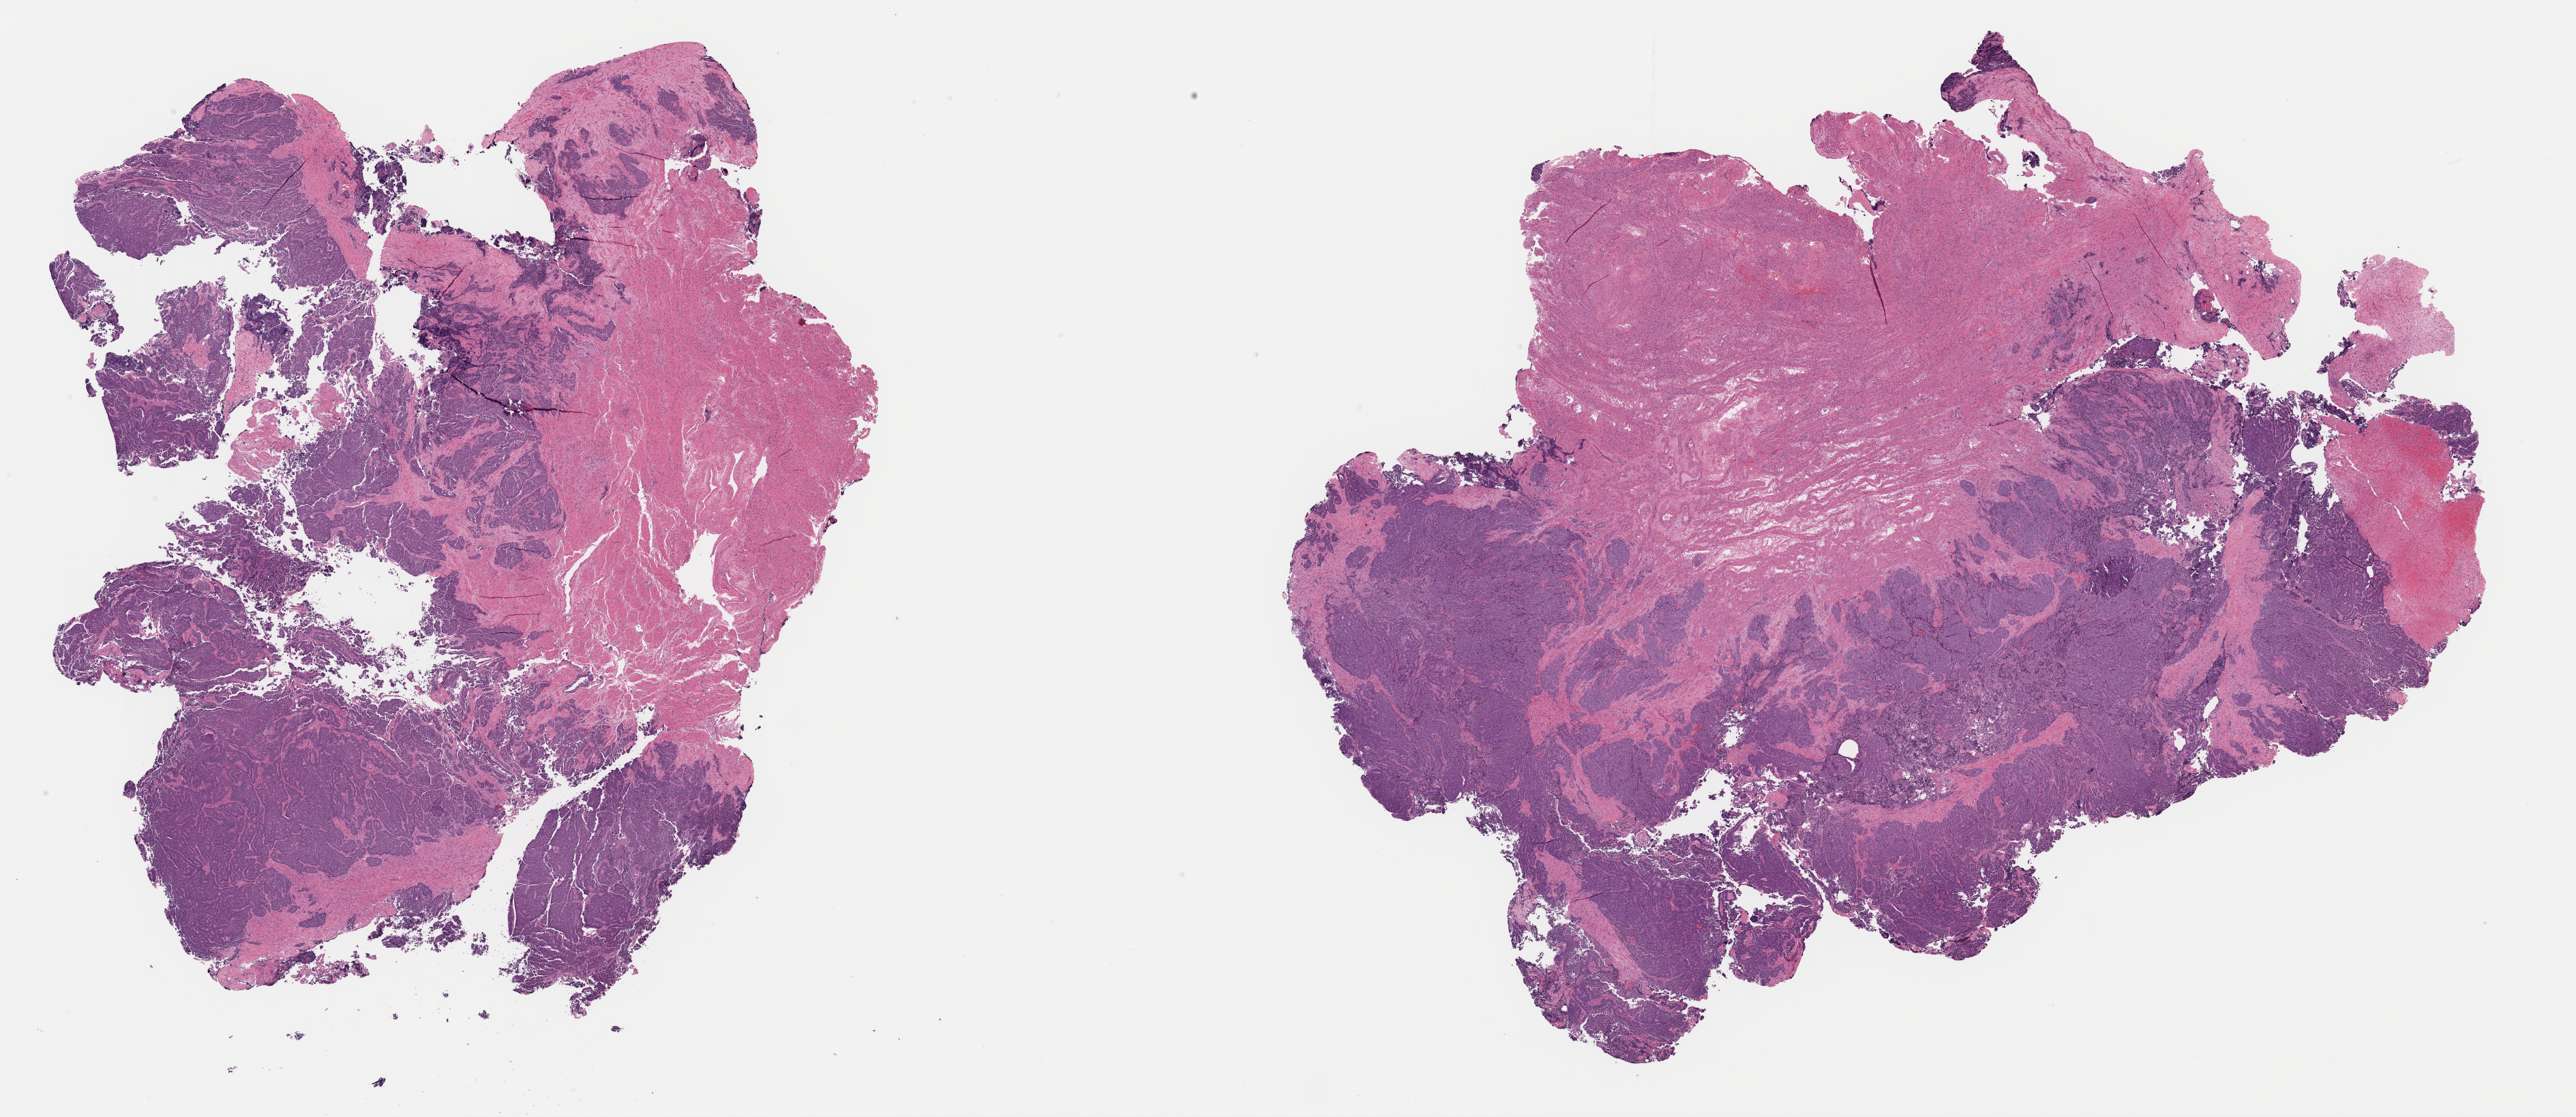
H&E whole-slide image, whole scanned area (about 29.8 x 12.9 mm, slide scanned at 40x) shown as a low-resolution overview. Formalin-fixed paraffin-embedded (FFPE) diagnostic section. Primary tumour sample from the uterus. Patient: female, age at initial diagnosis 81 years. Histologic grade: G3 (poorly differentiated).
FIGO stage: IVB. Histologic diagnosis: Endometrioid adenocarcinoma, NOS (endometrium).